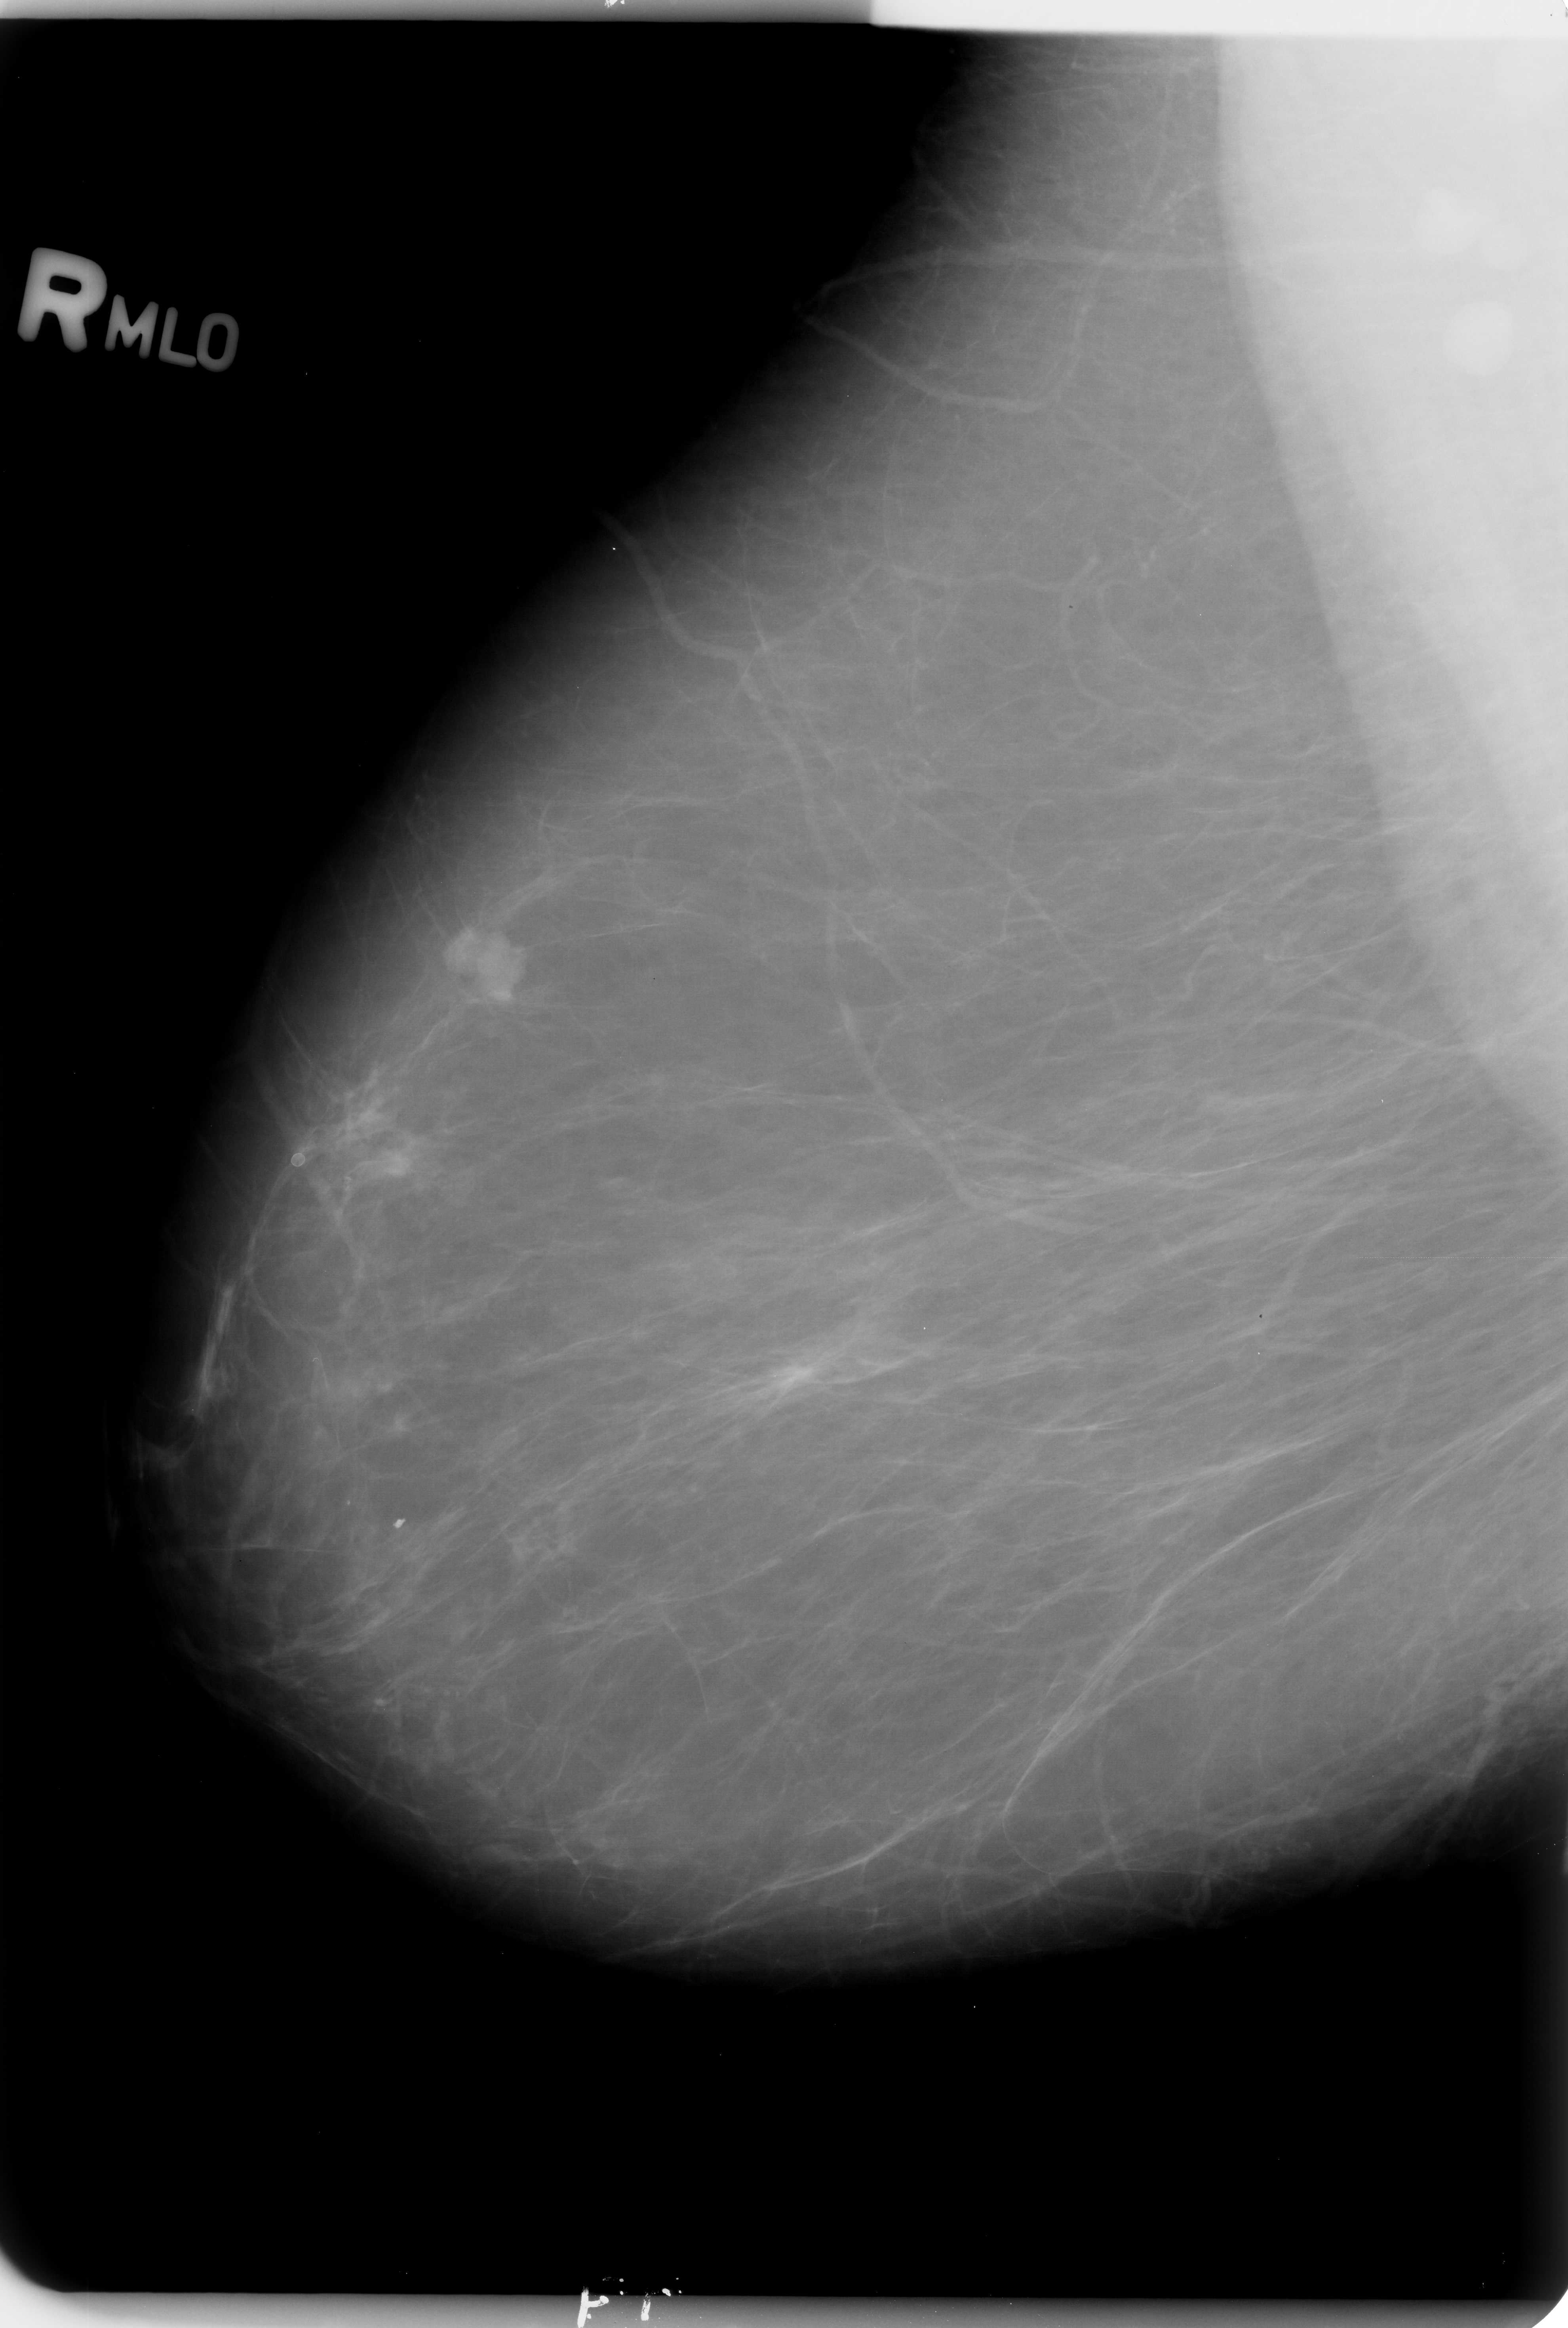
Scanned film-screen mammogram; right breast; MLO view.
Marked findings (only marked abnormalities are described; nothing is implied about the rest of the image): mass, shape lobulated, margins circumscribed / ill defined; BI-RADS assessment category 4; subtlety rating 5 on a 1 (subtle) to 5 (obvious) scale; pathology (as recorded): benign.